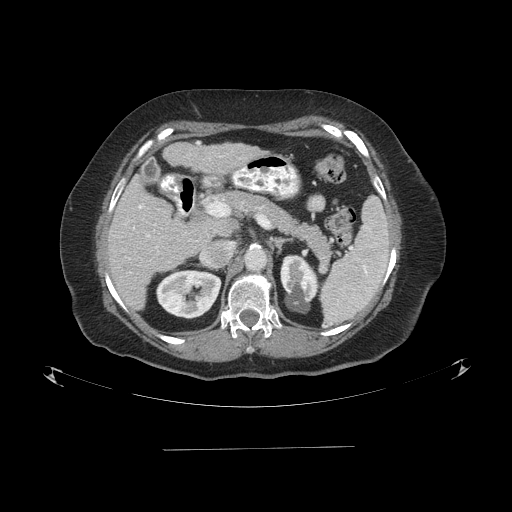
Contrast-enhanced abdominal CT (liver protocol), one axial slice; slice 45 of 103 in the series (ordered by position); reconstruction kernel STANDARD; one of 2 acquisitions stored at this slice position; soft-tissue window (W 400 / L 40 HU); 2.5 mm slice thickness; 512 × 512 image matrix, field of view 500 × 500 mm. Case-level facts recorded for this patient, not image findings: diagnosis: hepatocellular carcinoma (patient treated with transarterial chemoembolisation; whether this scan precedes or follows treatment is not stated here); TNM stage (as recorded): Stage-IIIA; Child-Pugh class: A; tumour differentiation: poorly differentiated; tumour nodularity: multinodular.
Annotated regions visible in this slice (semi-automatically segmented with operator editing):
- liver parenchyma outside the tumour (the mass and vessels are separate outlines, so this box may not span the whole liver): box from (x=108, y=176) to (x=206, y=308) px
- liver vessels: (x=139, y=205)–(x=156, y=237)